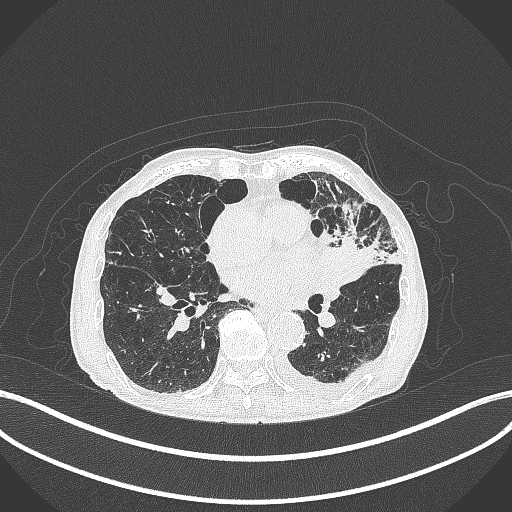
Chest CT, one axial slice; 120 kVp; lung window (W 1500 / L -600 HU); 512 × 512 image matrix, field of view 400 × 400 mm. Patient: male, 90 years or older. From the clinical record (not read from this slice): clinical TNM (as recorded): T2b N1 M0.
Structures marked on this image (bounding box drawn by a radiologist):
- lung tumour (recorded histology: squamous cell carcinoma): box from (x=315, y=239) to (x=375, y=287) px